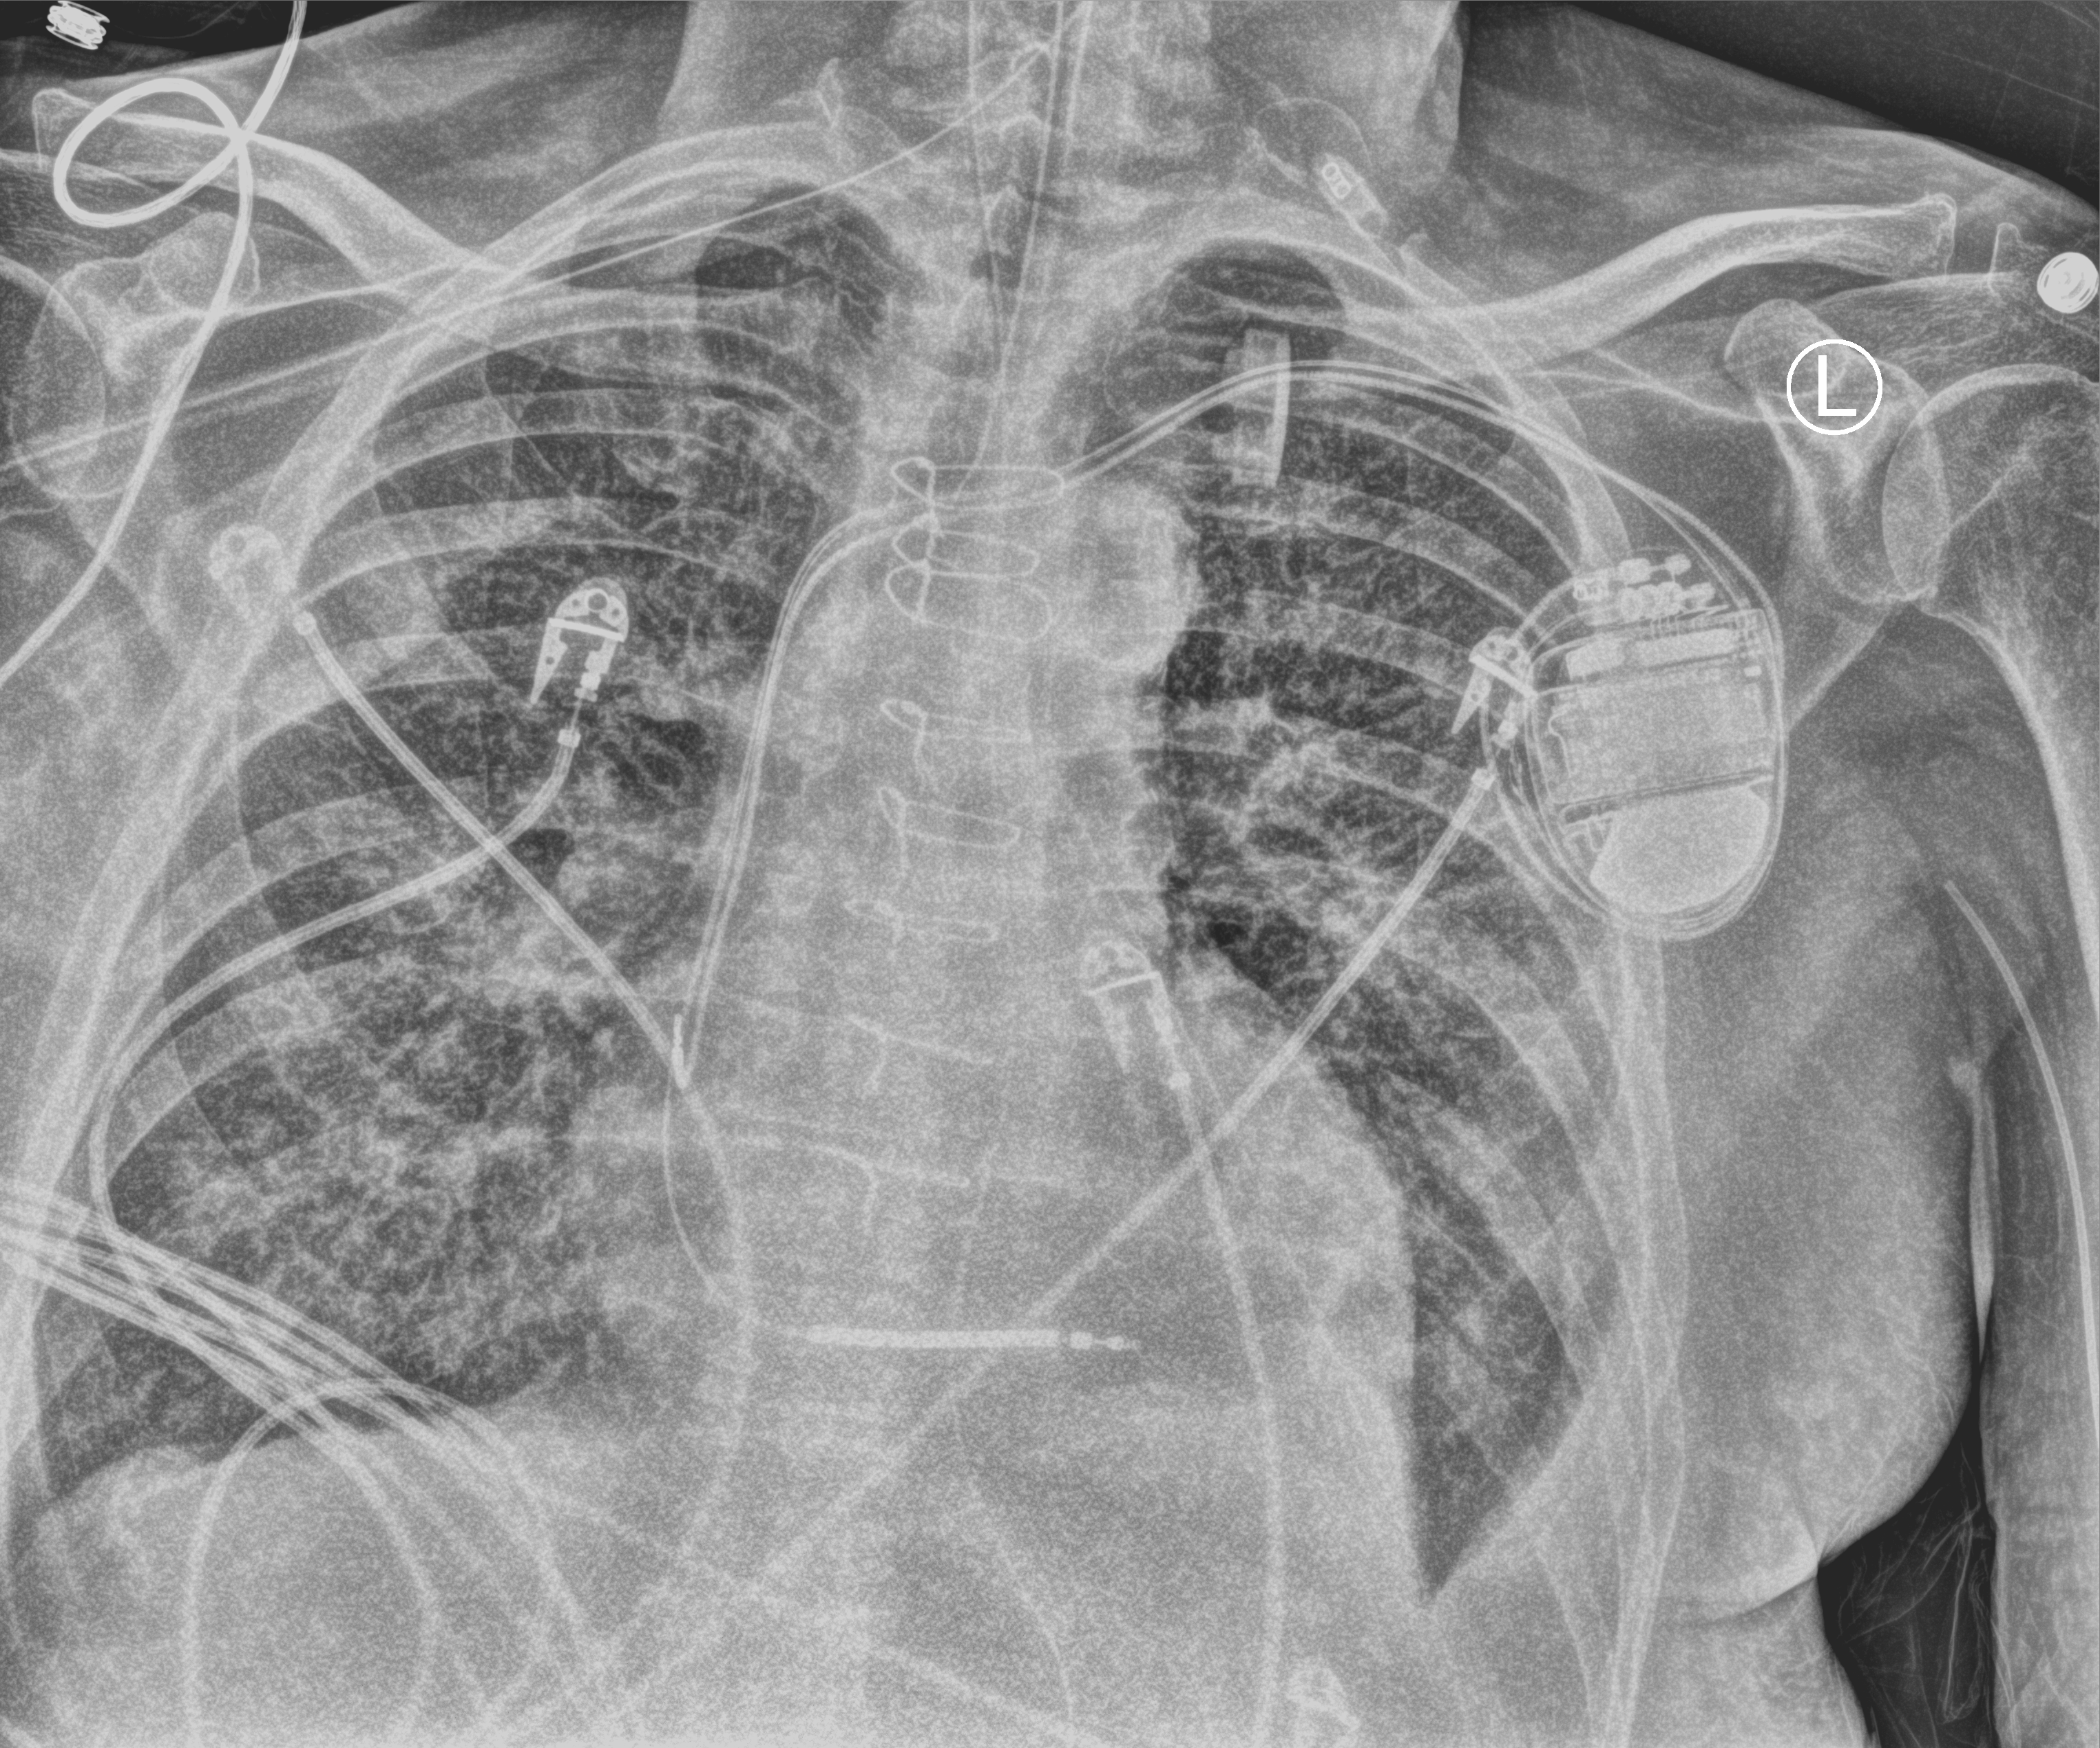
Bedside chest radiograph (computed radiography); anteroposterior (AP) projection. Patient hospitalised with COVID-19; male, aged 75–90 years.
From the hospital-stay record, not from the radiograph (when in the stay this image was taken is not recorded): mechanically ventilated during this hospital stay: yes; length of hospital stay: 11 days.